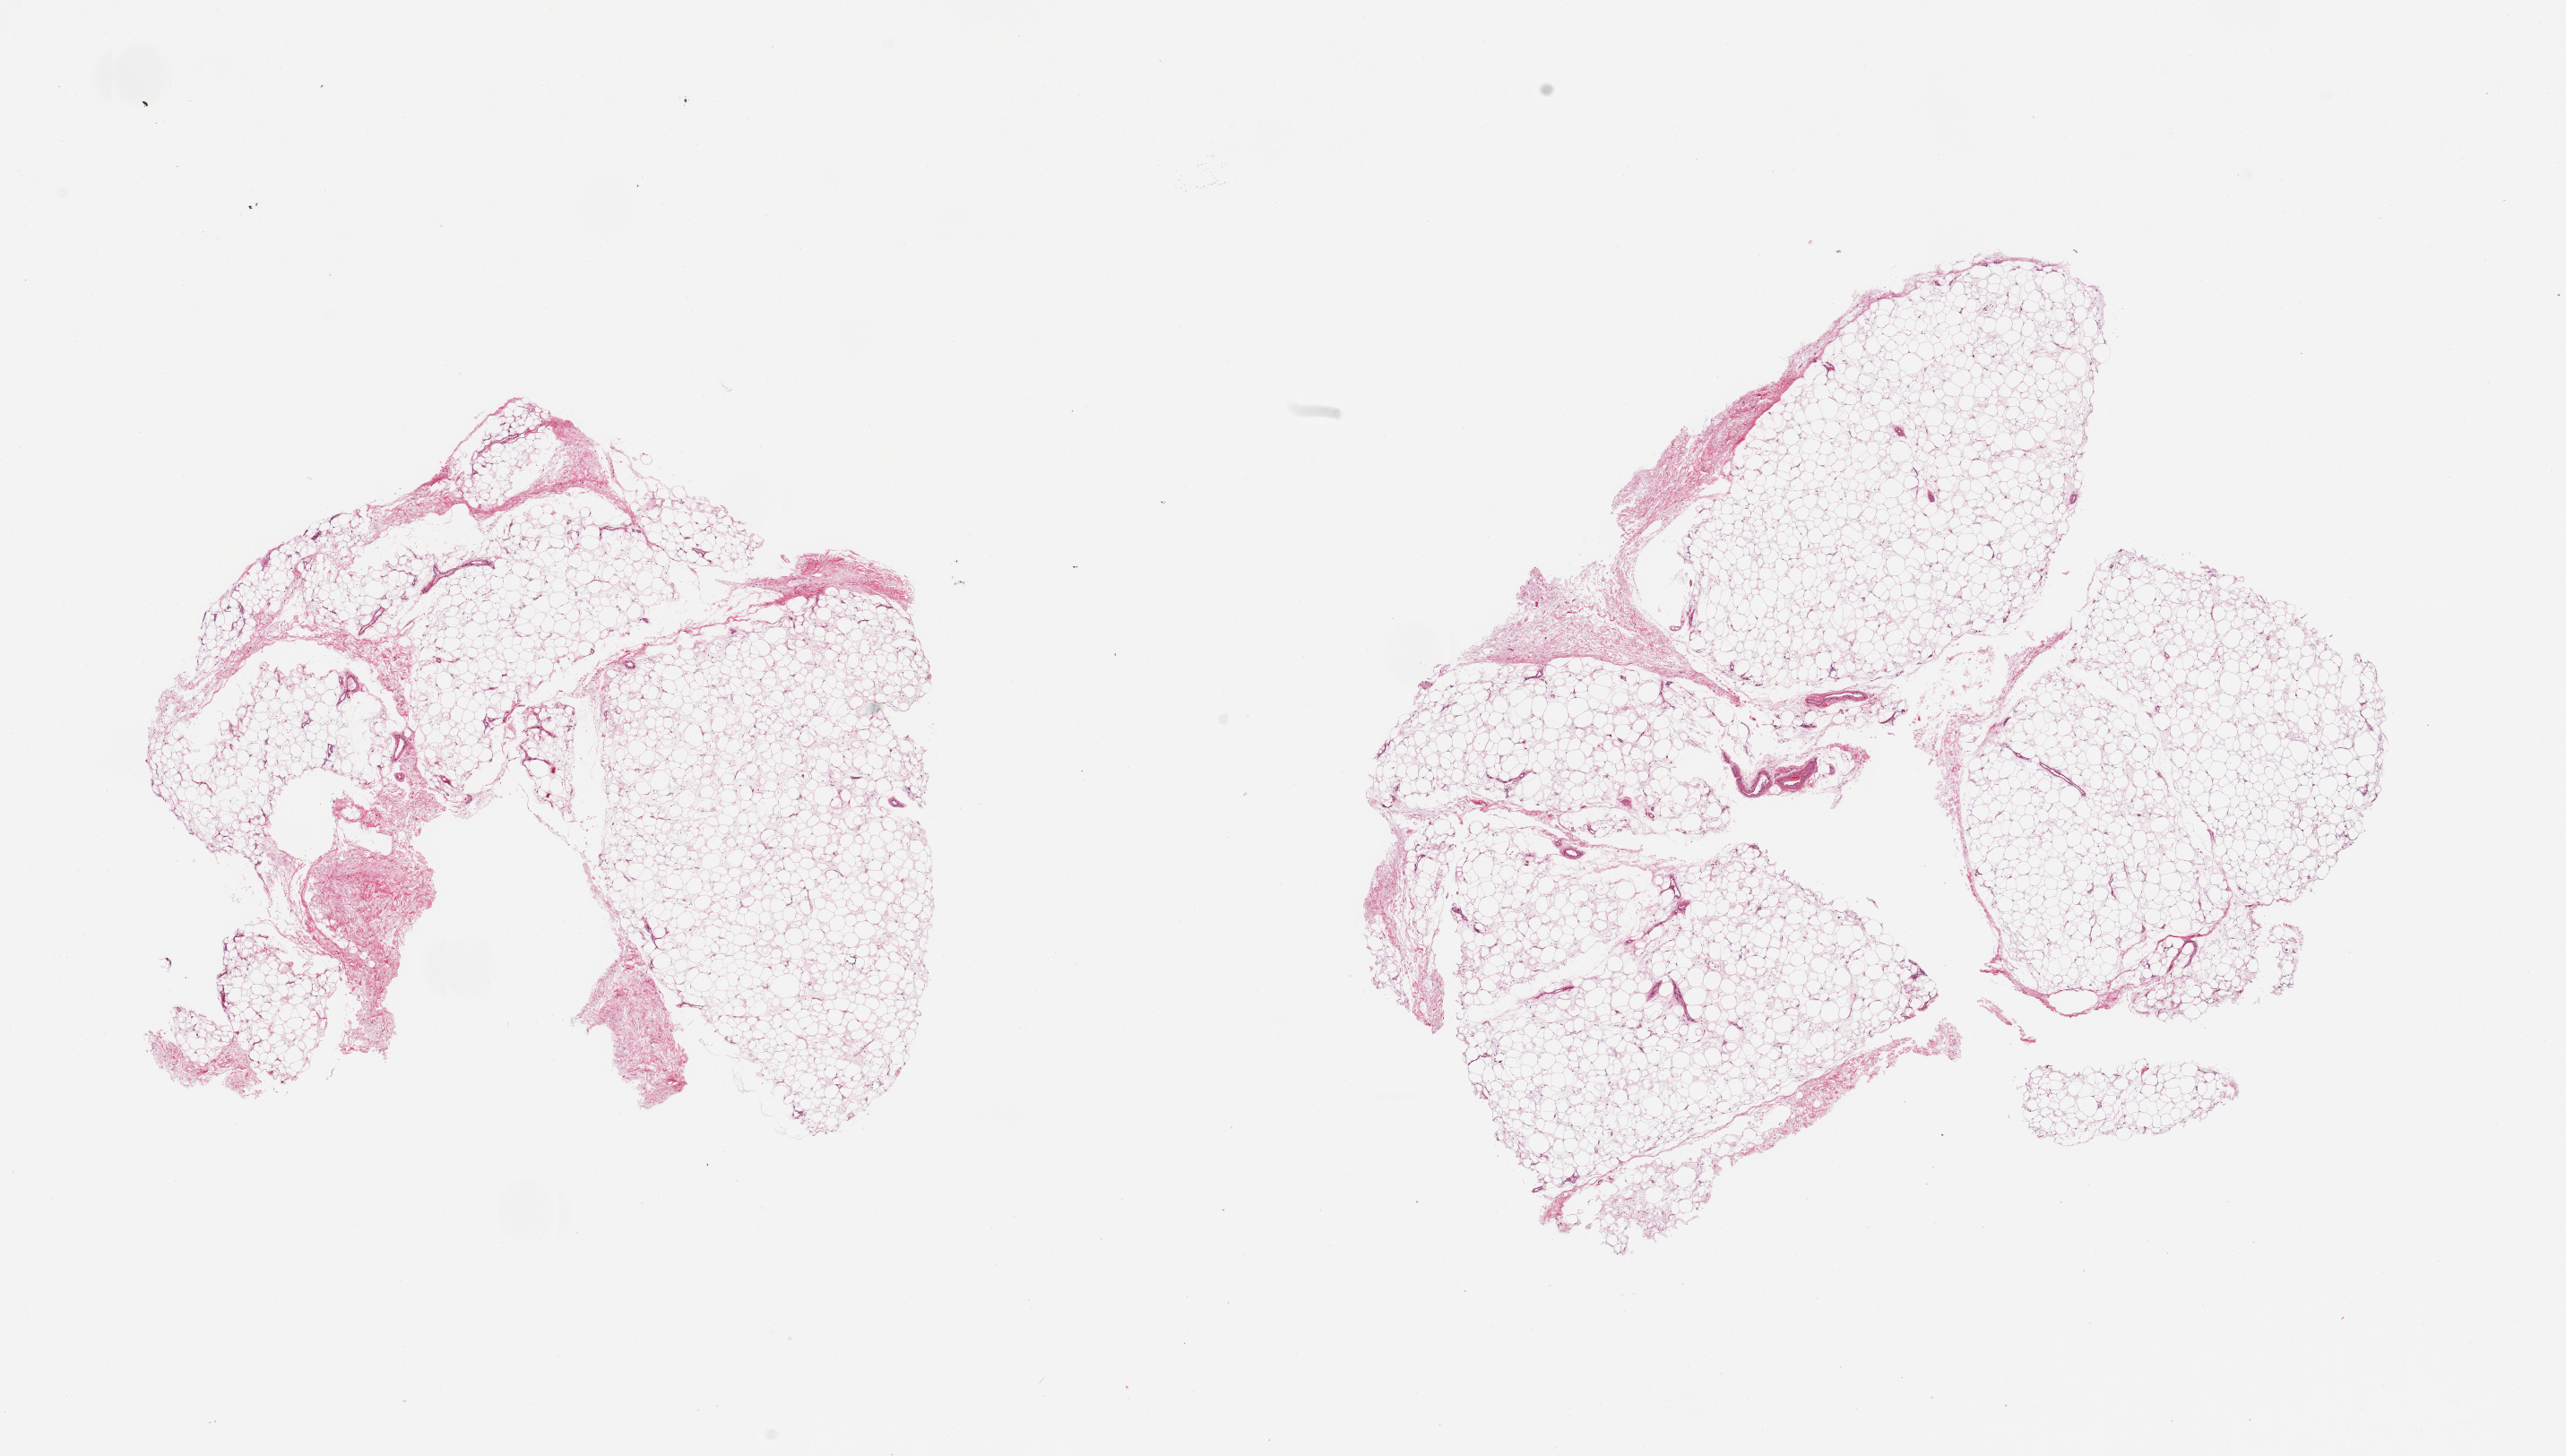
Whole-slide image, H&E stain, brightfield — low-resolution overview of the scanned area, about 22.6 x 12.9 mm, PAXgene-fixed, paraffin-embedded tissue, section of adipose tissue (target tissue), tissue donor sample.
Pathologist's review note for this sample: 2 pieces, ~5-10% fascia.